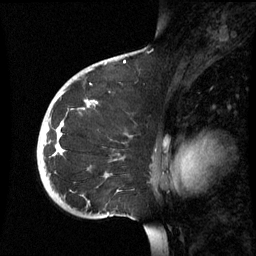
Breast MRI (dynamic contrast-enhanced), one sagittal slice; dynamic contrast-enhanced series, image 2 of 3 at this slice position (ordered by acquisition); 1.5 T; TE 4.2 ms, TR 8.9 ms; 256 × 256 image matrix. Patient: female, 35 years. From the clinical record (not read from this slice): setting: breast cancer imaged before/during neoadjuvant chemotherapy; receptor status: HR-positive, HER2-negative.
Annotated regions visible in this slice (semi-automatically segmented with operator editing):
- analysis volume of interest (the breast-tissue region the enhancement analysis was run in; not a lesion): bounding box (x1, y1, x2, y2) in pixels: (37, 74, 163, 219)
- tumour enhancement mask (voxels above the 70 % enhancement threshold inside the analysis volume of interest): (57, 102, 93, 153)